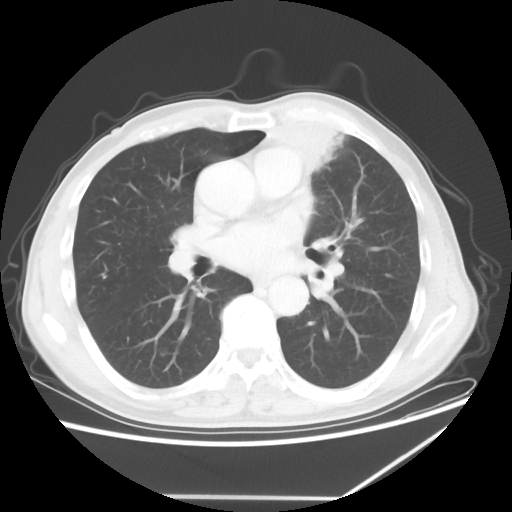
Chest CT, one axial slice. Slice 32 of 64 in the series (ordered by position). Lung window (W 1500 / L -600 HU). 5 mm slice thickness. 512 × 512 image matrix. Patient: male, 64 years. Case-level facts recorded for this patient, not image findings: clinical TNM (as recorded): T1c N1 M1; histopathological grade: G2.
Annotated regions visible in this slice (rectangle marked by the reading radiologist):
- lung tumour (recorded histology: squamous cell carcinoma): box from (x=267, y=119) to (x=348, y=209) px